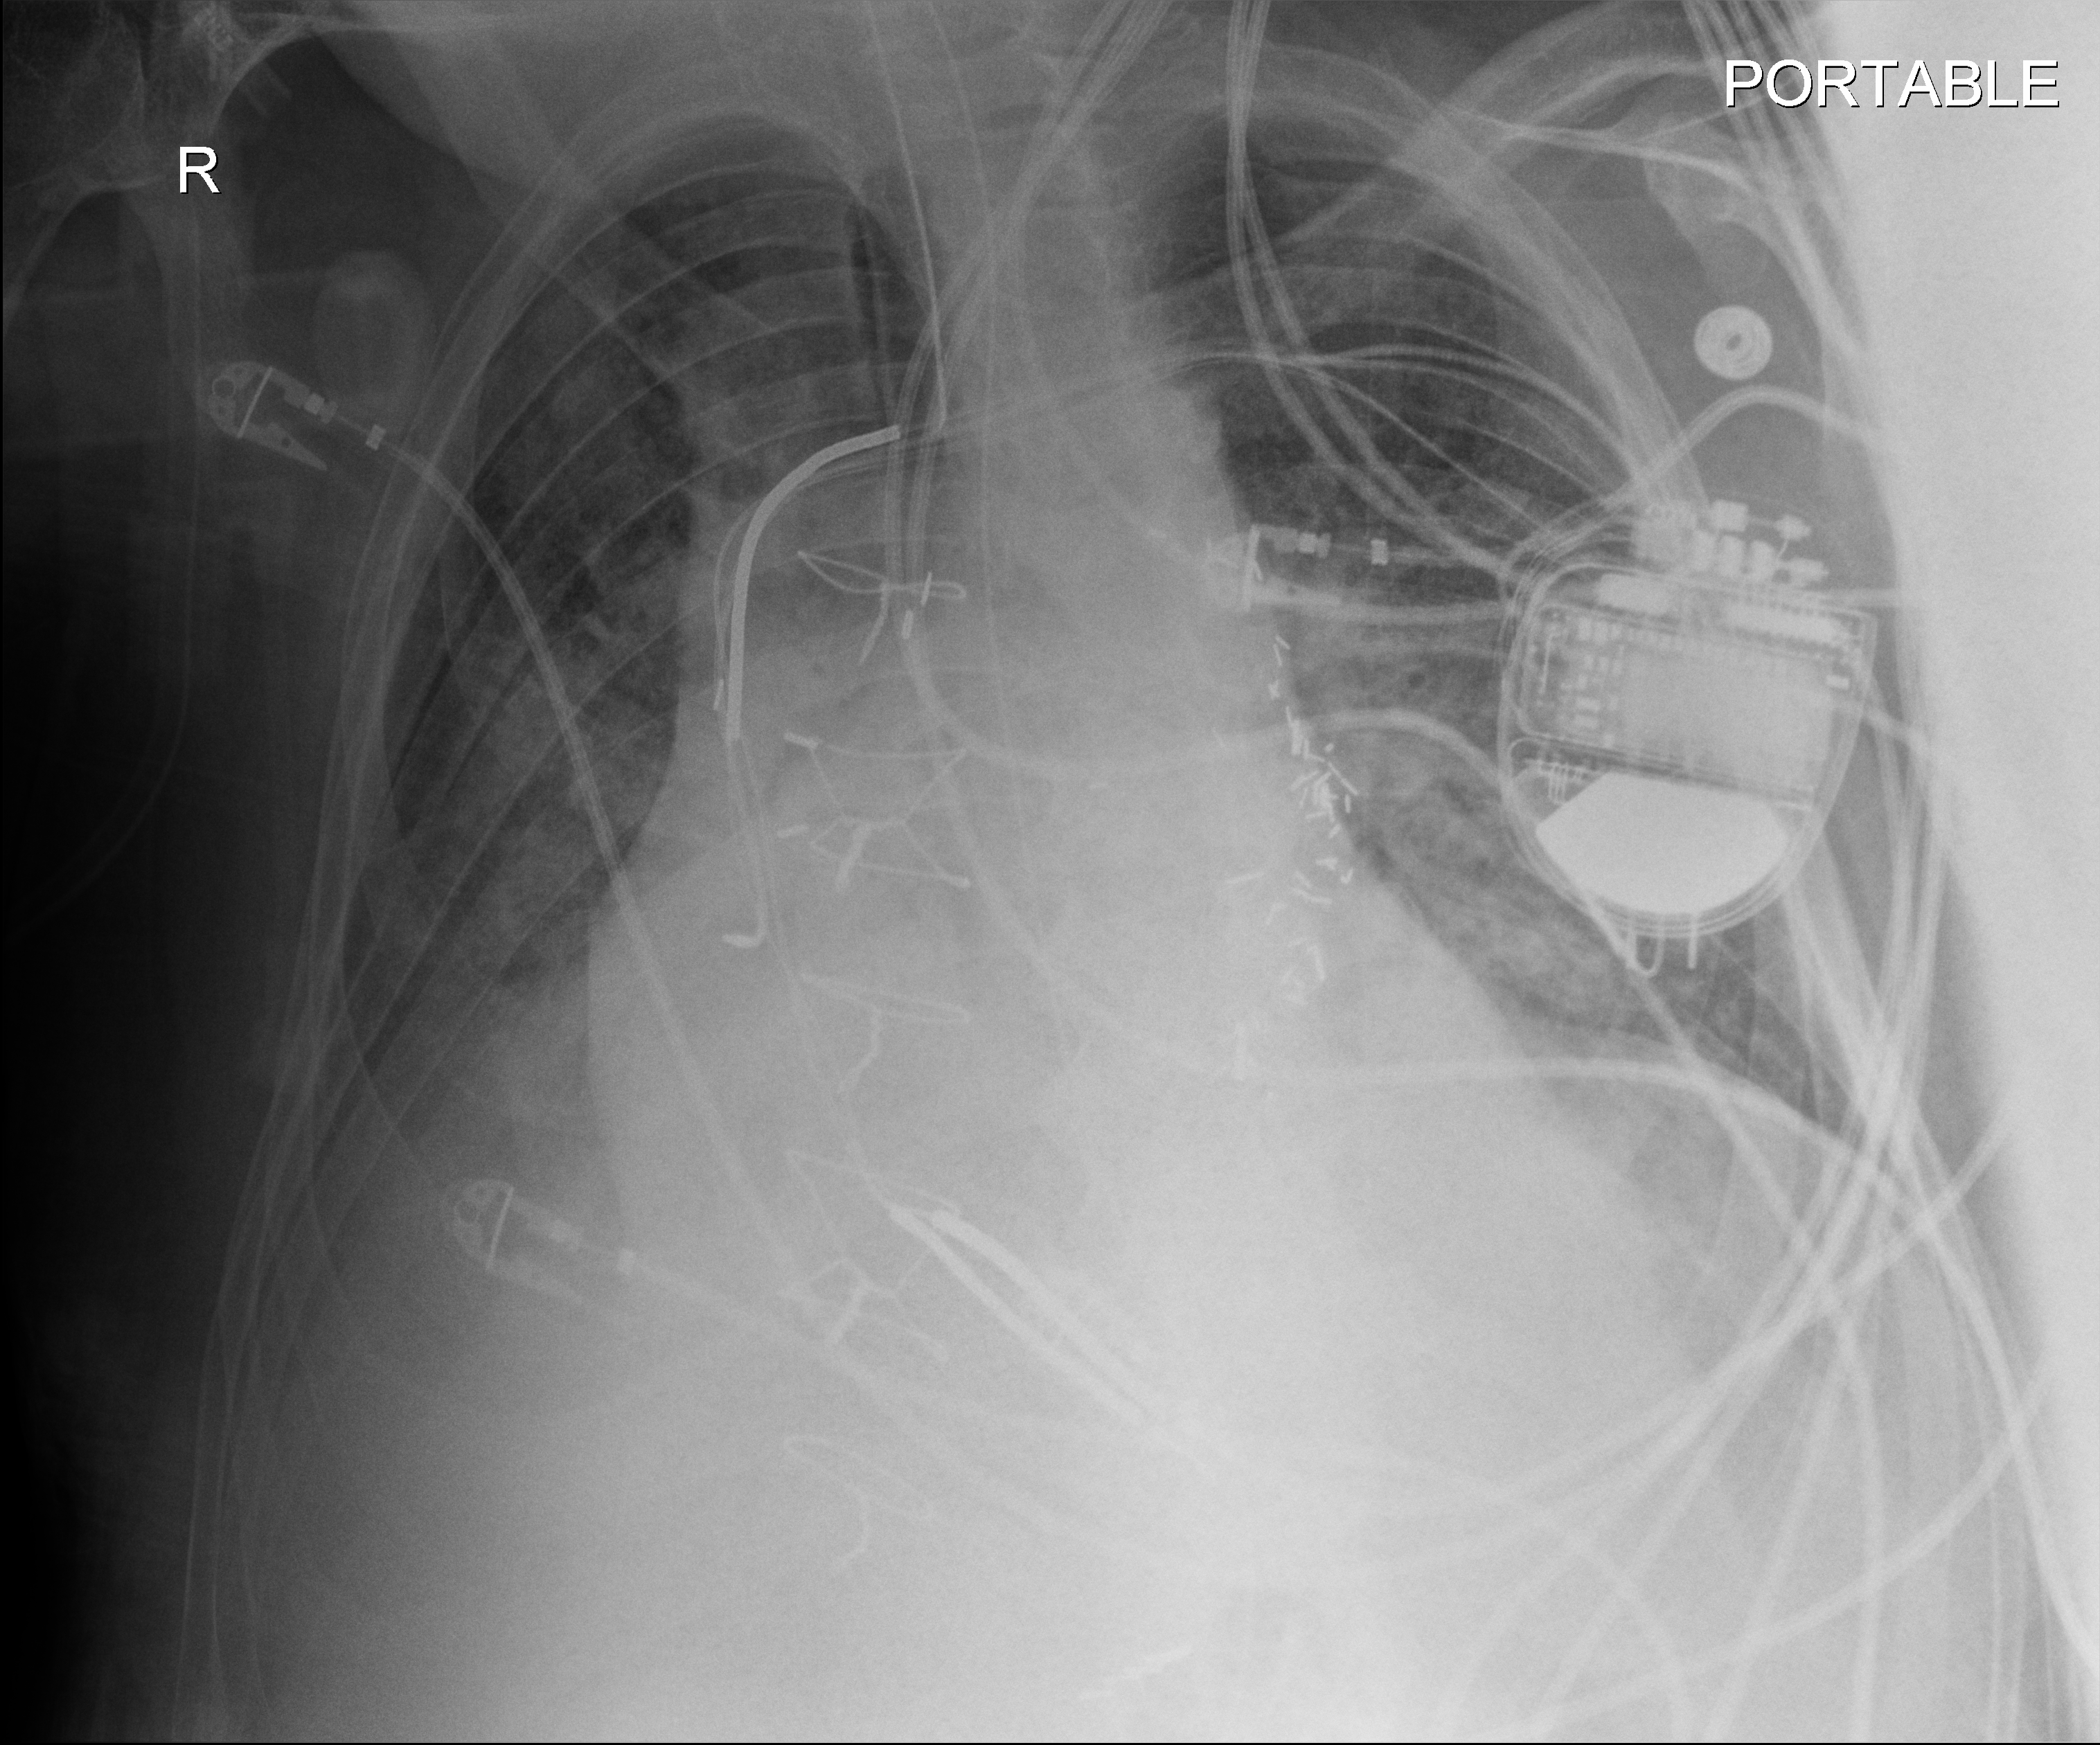
Bedside chest radiograph (digital radiography), anteroposterior (AP) projection. Patient hospitalised with COVID-19; male, aged 60–74 years.
Admission-level facts for this patient (not findings on this image; timing relative to this image not recorded): length of hospital stay: 55 days; mechanically ventilated during this hospital stay: yes; chronic kidney disease (admission record): no.